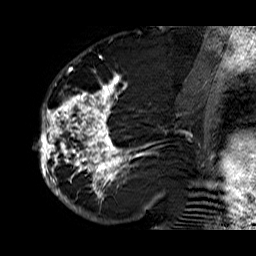
Breast MRI (dynamic contrast-enhanced), one sagittal slice; slice 33 of 60 in the series (ordered by position); dynamic contrast-enhanced series, time point 2 of 6 at this slice position (early post-contrast); 1.5 T; TE 6.3 ms, TR 32.9 ms; 4 mm slice thickness; 256 × 256 image matrix, field of view 200 × 200 mm. Female patient. From the clinical record (not read from this slice): setting: breast cancer imaged before/during neoadjuvant chemotherapy; receptor status: HR-positive, HER2-negative.
Annotated regions visible in this slice (semi-automatic segmentation, software-assisted and operator-edited):
- analysis volume of interest (the breast-tissue region the enhancement analysis was run in; not a lesion): box from (x=33, y=74) to (x=176, y=210) px
- tumour enhancement mask (voxels above the 100 % enhancement threshold inside the analysis volume of interest): (x=37, y=74)–(x=152, y=210)